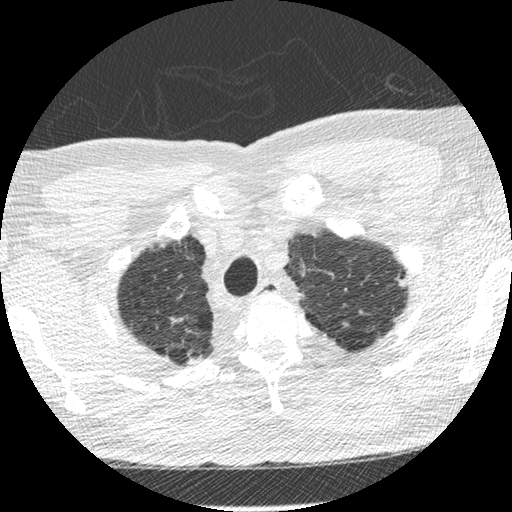
Low-dose screening chest CT, one axial slice. Slice 246 of 275 in the series (ordered by position). 120 kVp. Lung window (W 1500 / L -600 HU). 512 × 512 image matrix.
Annotated regions visible in this slice (expert manual segmentation):
- lesion 1 (tumor, upper lobe of left lung): bounding box <397,276,406,287> (left, top, right, bottom; pixels)